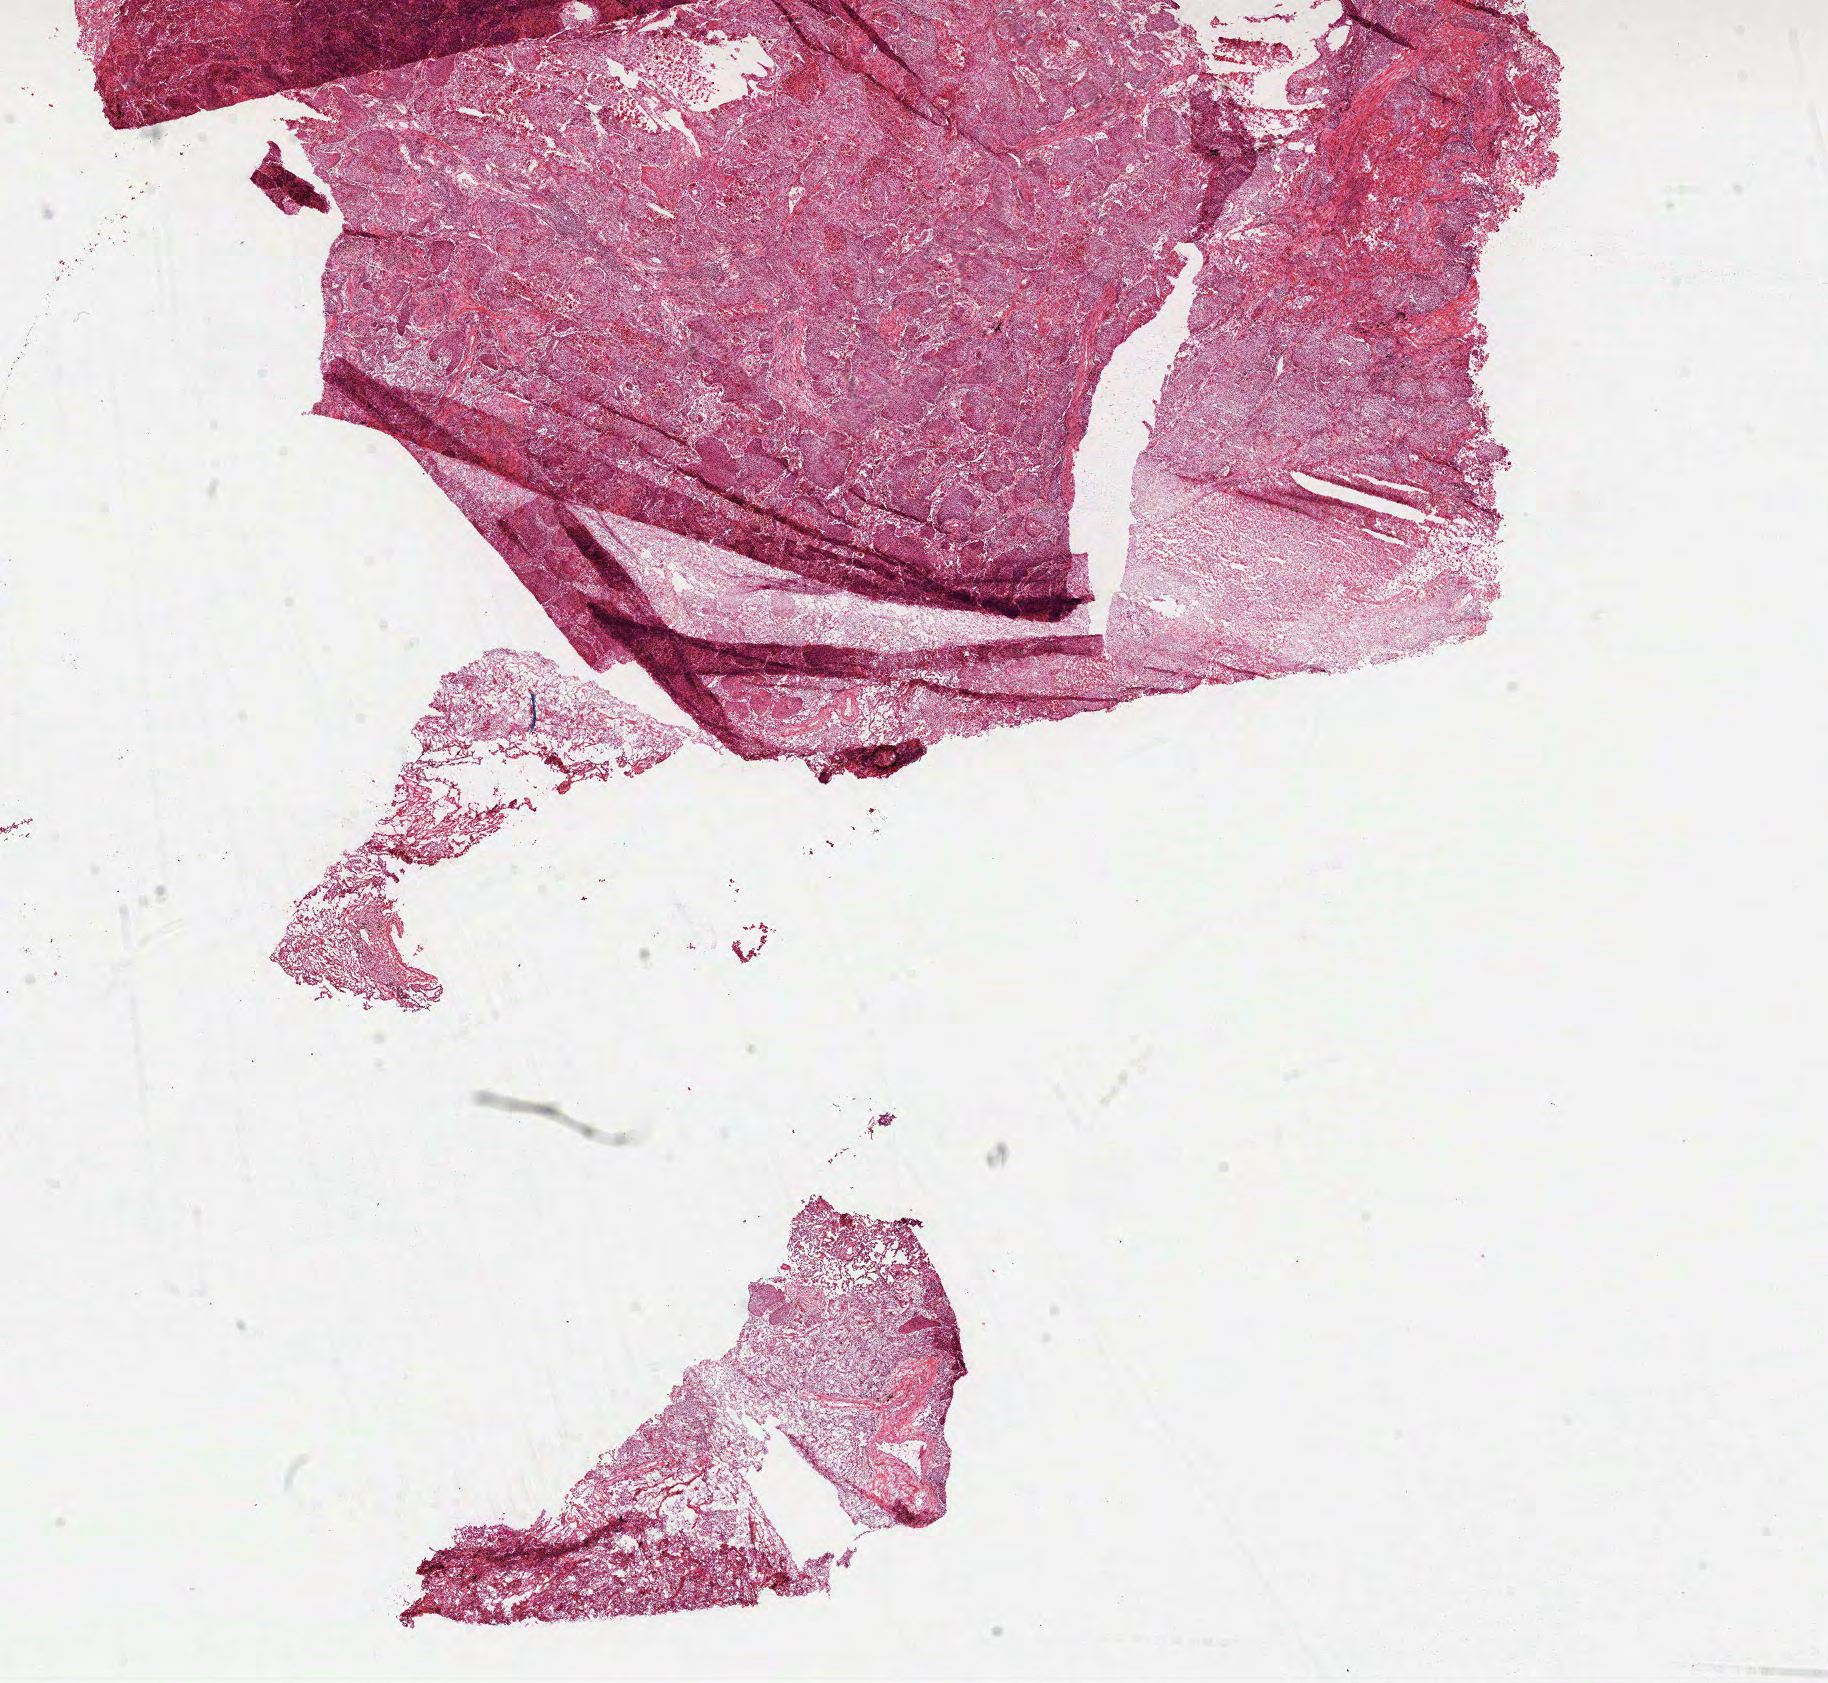
Whole-slide histology image, Hematoxylin and eosin (H&E) stained, whole scanned area (about 14.7 x 13.6 mm) shown as a low-resolution overview. Formalin-fixed paraffin-embedded (FFPE) diagnostic section. Lung, primary tumour sample. Male patient; age at initial diagnosis 64 years.
AJCC pathologic stage: IIB. Histologic diagnosis: Squamous cell carcinoma, NOS (upper lobe, lung).